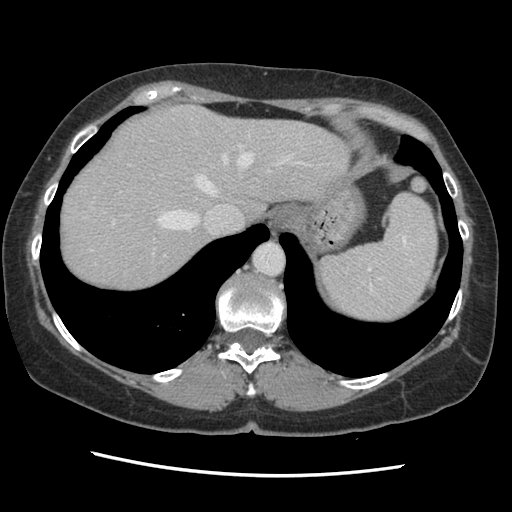
Contrast-enhanced abdominal CT, one axial slice; slice 112 of 141 in the series (ordered by position); 120 kVp; soft-tissue window (W 400 / L 40 HU); 512 × 512 image matrix, field of view 330 × 330 mm. Female patient, age 61 years. From the clinical record (not read from this slice): diagnosis: colorectal cancer liver metastases, imaged before liver resection; multiple liver metastases: no; largest metastasis: 2.4 cm; disease in both lobes: no.
Structures marked on this image (outlined manually by an expert reader):
- hepatic veins: bounding box (x1, y1, x2, y2) in pixels: (153, 144, 307, 254)
- liver: (60, 105, 349, 294)
- planned liver remnant (the part of the liver to remain after resection): (60, 105, 349, 293)
- portal vein (with intrahepatic branches): (112, 221, 166, 256)